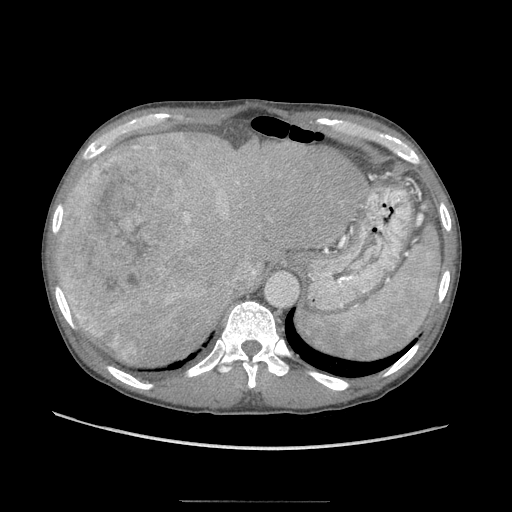
Contrast-enhanced abdominal CT (liver protocol), one axial slice. Position 72 of 103 along the scan axis. Reconstruction kernel STANDARD. Soft-tissue window (W 400 / L 40 HU). 2.5 mm slice thickness. 512 × 512 image matrix, field of view 380 × 380 mm. Case-level facts recorded for this patient, not image findings: diagnosis: hepatocellular carcinoma (patient treated with transarterial chemoembolisation; whether this scan precedes or follows treatment is not stated here); TNM stage (as recorded): Stage-IIIA; Child-Pugh class: A; tumour nodularity: multinodular.
Outlined on this slice (semi-automatically segmented with operator editing):
- liver parenchyma outside the tumour (the mass and vessels are separate outlines, so this box may not span the whole liver): box from (x=56, y=136) to (x=367, y=366) px
- mass: (x=57, y=142)–(x=189, y=361)
- liver vessels: (x=145, y=147)–(x=204, y=302)